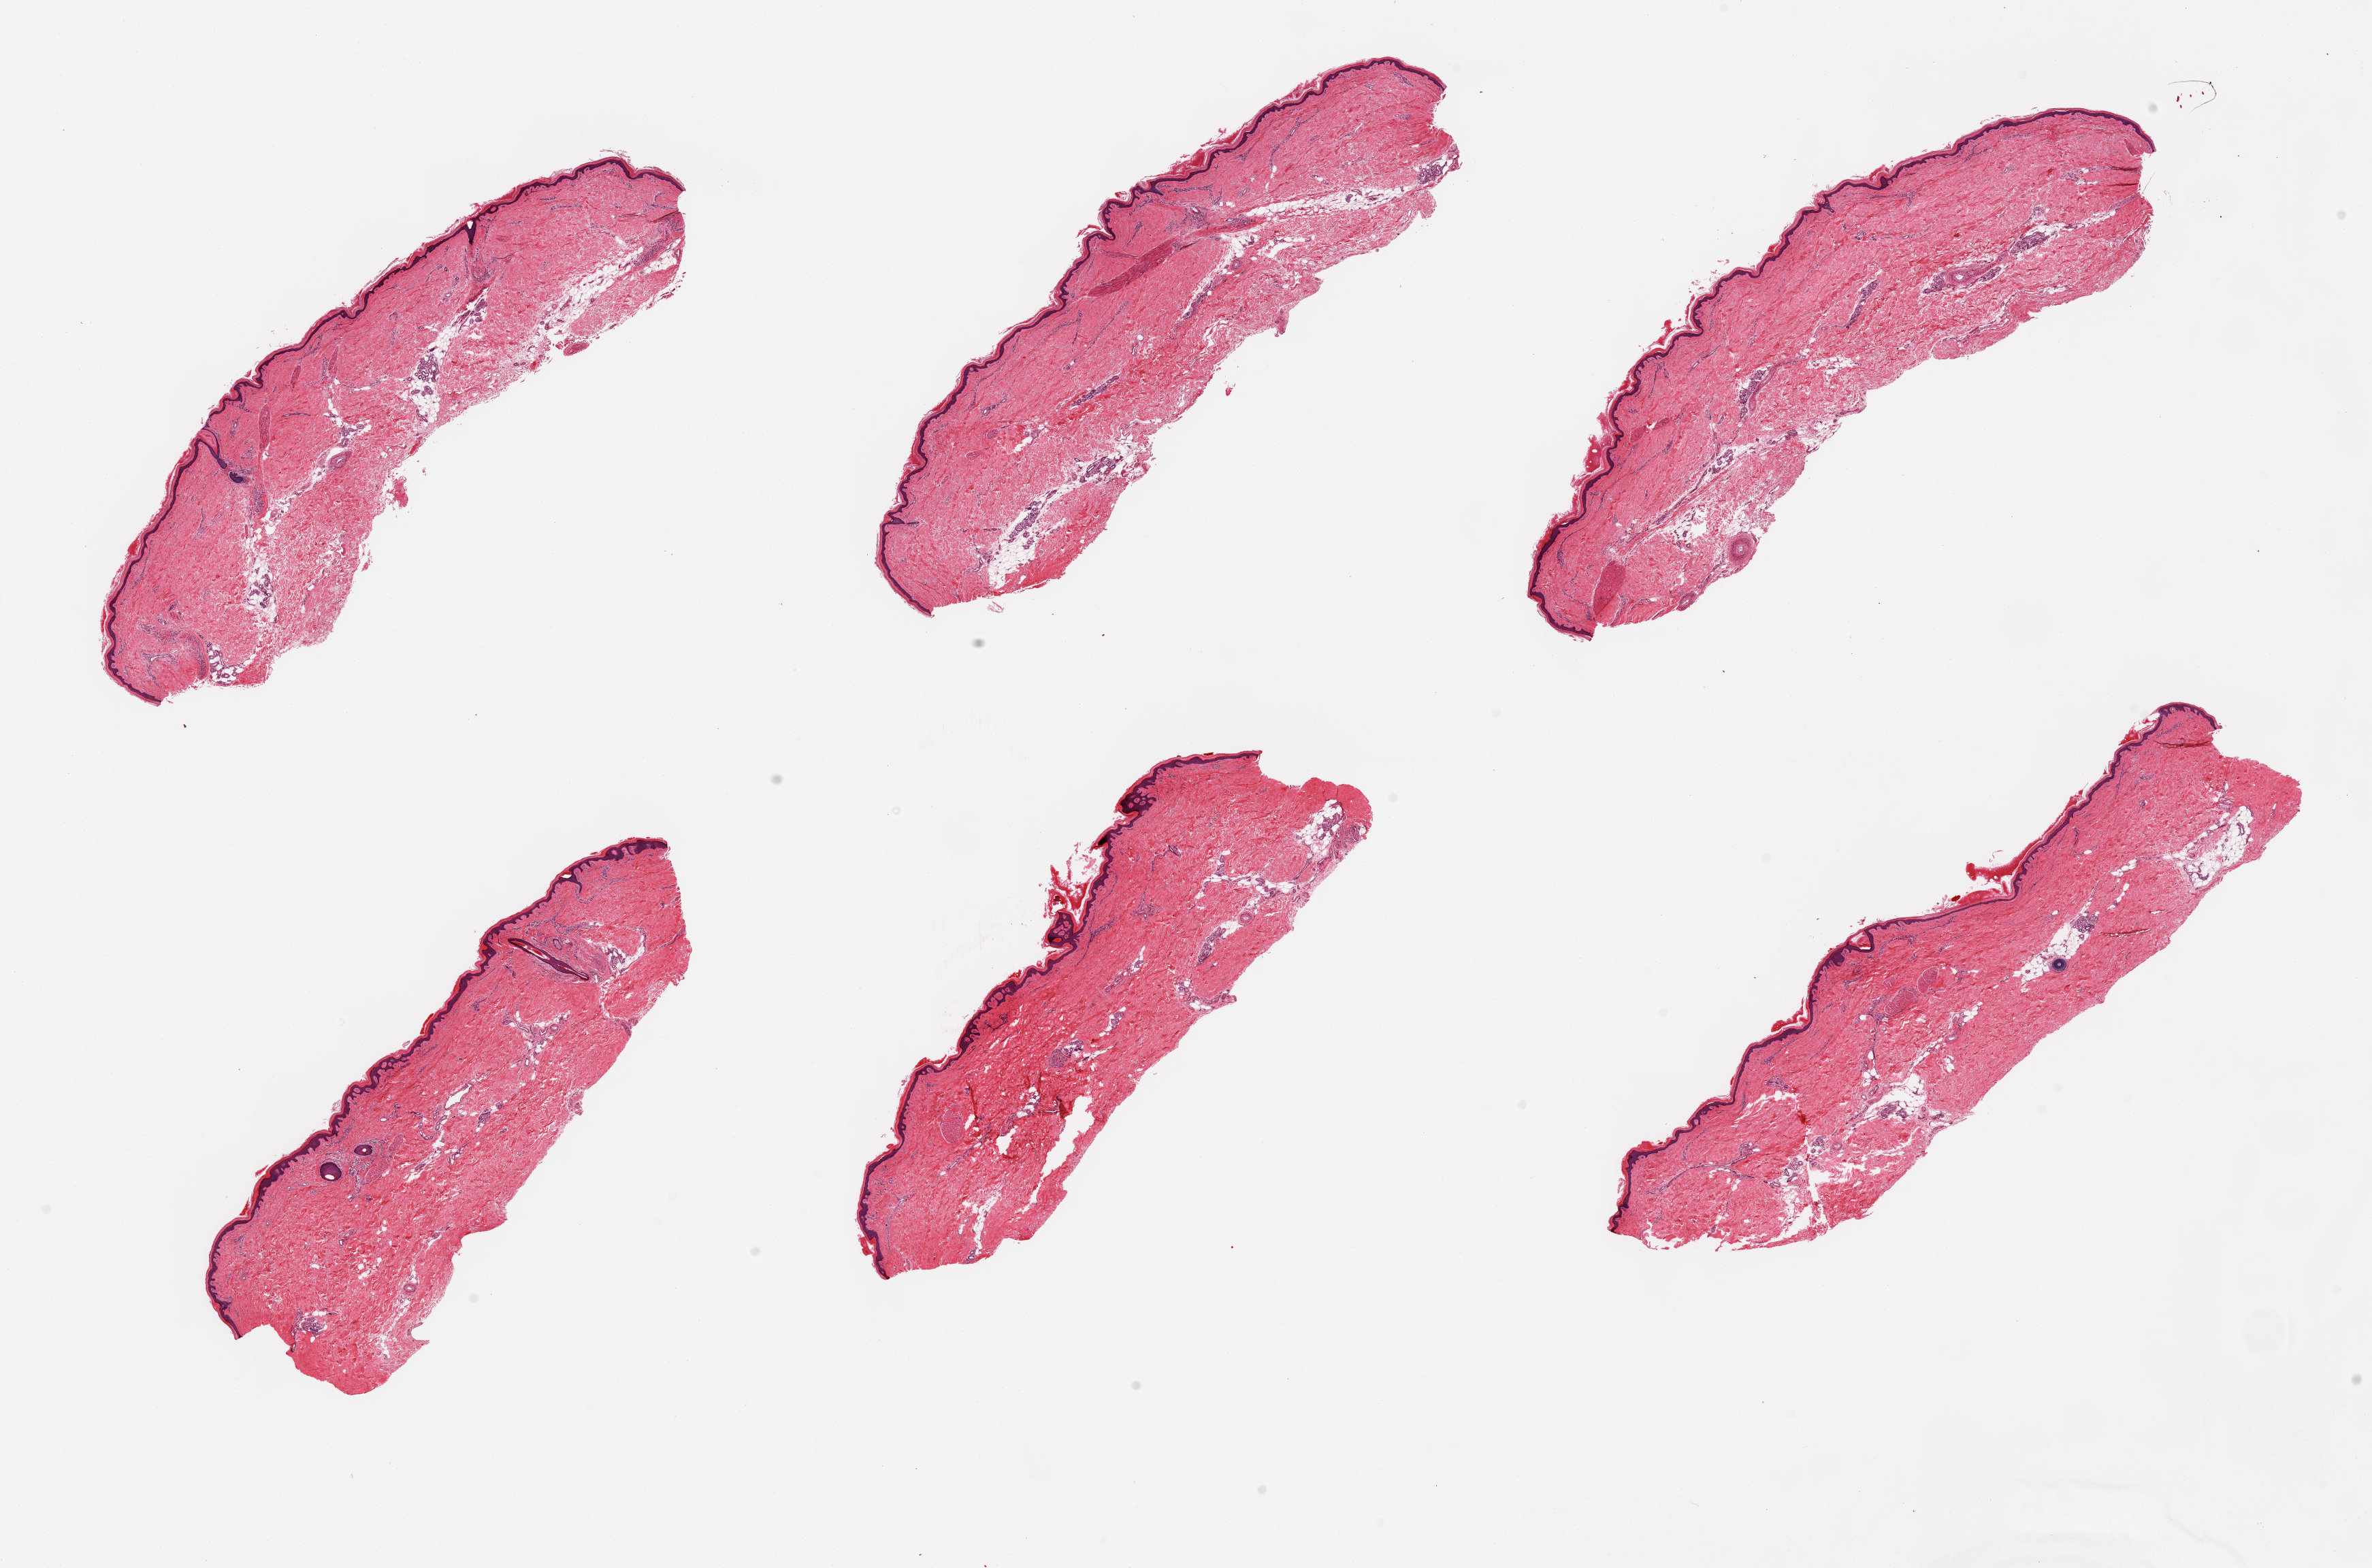
Digitized H&E-stained section — shown as a low-resolution overview of the whole scanned area (about 27.6 x 18.2 mm, from a 20x scan). PAXgene-fixed, paraffin-embedded tissue. Sampled site (target tissue): skin of lower leg. Donor tissue sample.
Pathologist's review note for this sample: 6 pieces; well trimmed with minimal internal fat, epidermis measures 38 microns.